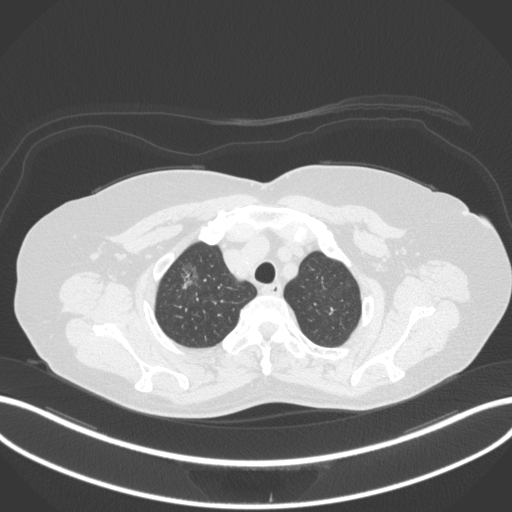
Chest CT, one axial slice. Lung window (W 1500 / L -600 HU). 1 mm slice thickness. 512 × 512 image matrix. Female patient, age 62 years. From the clinical record (not read from this slice): clinical TNM (as recorded): T1c N0 M0.
Structures marked on this image (rectangle marked by the reading radiologist):
- lung tumour (recorded histology: adenocarcinoma): bounding box <172,255,208,293> (left, top, right, bottom; pixels)